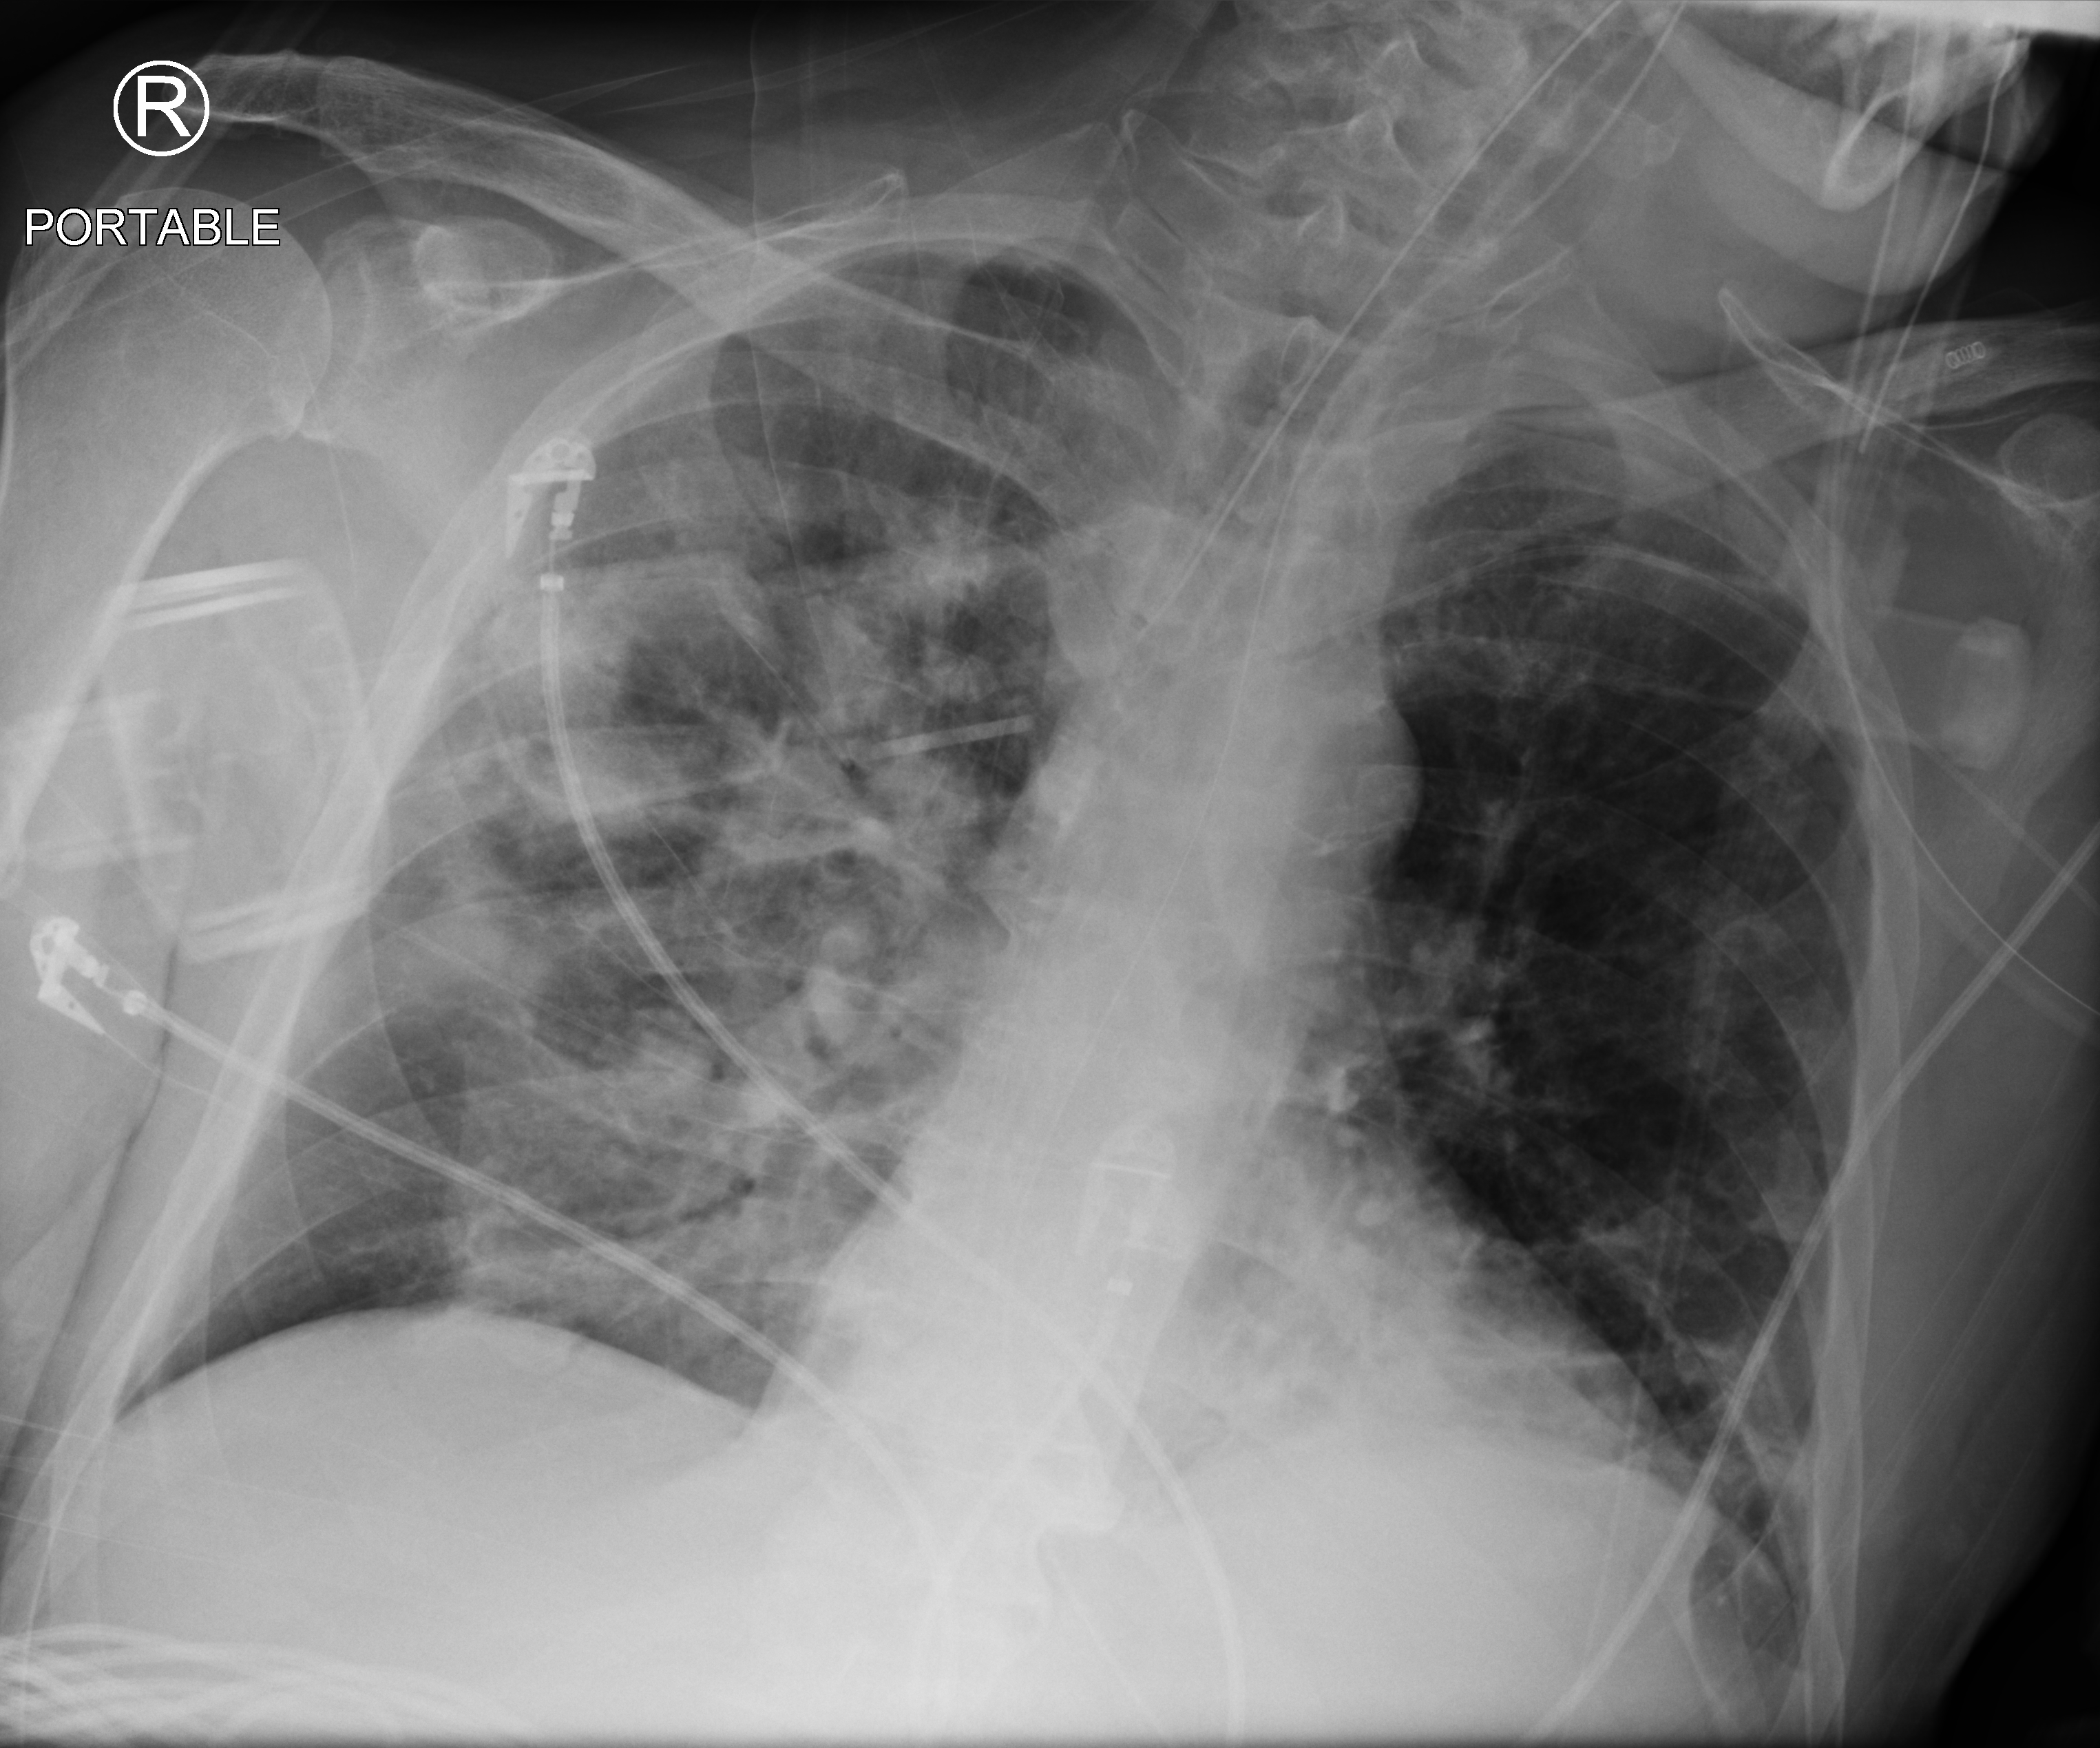
Portable chest radiograph, anteroposterior (AP) projection. Male patient hospitalised with COVID-19, age 60–74 years.
From the hospital-stay record, not from the radiograph (when in the stay this image was taken is not recorded):
- mechanically ventilated during this hospital stay: yes